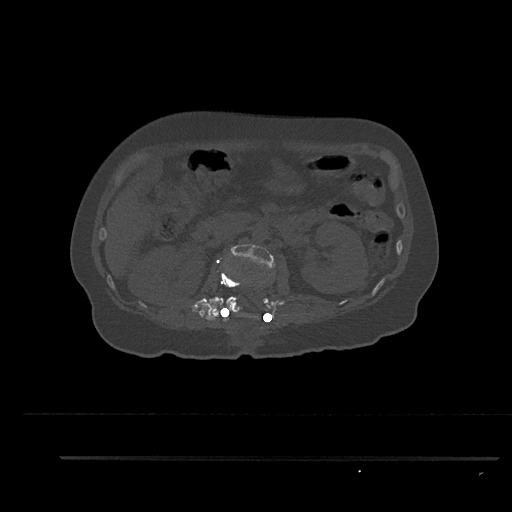
CT including the spine, one axial slice; slice 189 of 797 in the series (ordered by position); reconstruction kernel Br40s/3; 120 kVp; bone window (W 1800 / L 400 HU); 512 × 512 image matrix, field of view 408 × 408 mm. Patient: female, 44 years. Case-level facts recorded for this patient, not image findings: primary cancer: renal; vertebrae with lytic lesions (as recorded): L1.
Annotated regions visible in this slice (semi-automatically segmented with operator editing):
- L1 vertebra: bounding box <217,264,242,317> (left, top, right, bottom; pixels)
- L2 vertebra: <226,244,273,316>